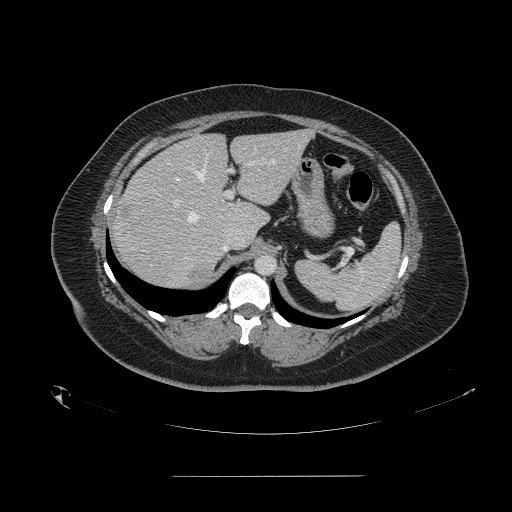
Contrast-enhanced abdominal CT, one axial slice. Position 106 of 164 along the scan axis. 120 kVp. Intravenous contrast given. Soft-tissue window (W 400 / L 40 HU). 2.5 mm slice thickness. 512 × 512 image matrix, field of view 495 × 495 mm. Female patient, age 52 years. Case-level facts recorded for this patient, not image findings: diagnosis: colorectal cancer liver metastases, imaged before liver resection.
Outlined on this slice (manually delineated by an expert):
- hepatic veins: bounding box [x1, y1, x2, y2] px = [187, 145, 299, 222]
- liver: [112, 131, 310, 289]
- planned liver remnant (the part of the liver to remain after resection): [174, 131, 310, 231]
- portal vein (with intrahepatic branches): [173, 161, 257, 207]
- liver metastasis: [190, 268, 212, 278]
- liver metastasis: [250, 209, 260, 221]
- liver metastasis: [119, 204, 131, 217]